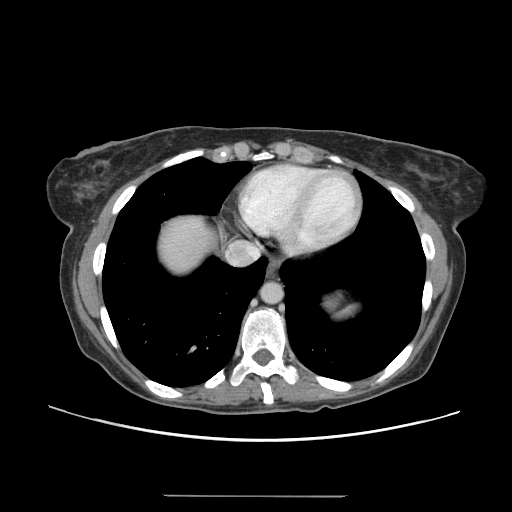
Contrast-enhanced abdominal CT, one axial slice. Position 134 of 144 along the scan axis. Intravenous contrast given. Soft-tissue window (W 400 / L 40 HU). 2.5 mm slice thickness. 512 × 512 image matrix, field of view 380 × 380 mm. Female patient, age 53 years. Case-level facts recorded for this patient, not image findings: diagnosis: colorectal cancer liver metastases, imaged before liver resection; multiple liver metastases: yes; largest metastasis: 1.1 cm; chemotherapy before resection: no.
Annotated regions visible in this slice (expert manual segmentation):
- hepatic veins: bounding box (x1, y1, x2, y2) in pixels: (249, 248, 258, 257)
- liver: (159, 214, 211, 274)
- planned liver remnant (the part of the liver to remain after resection): (155, 213, 217, 278)